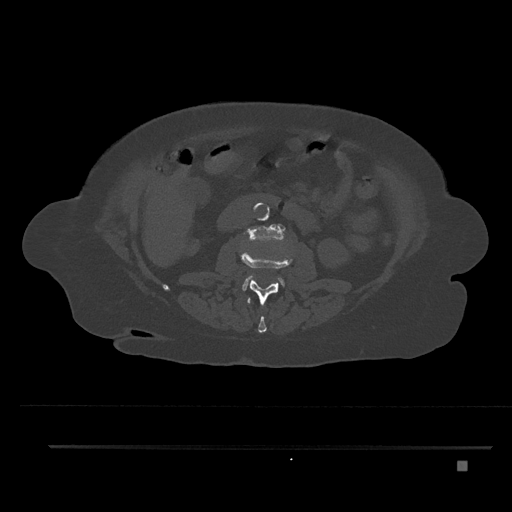
CT including the spine, one axial slice; position 167 of 797 along the scan axis; bone window (W 1800 / L 400 HU); 0.5 mm slice thickness; 512 × 512 image matrix, field of view 437 × 437 mm. Female patient, age 76 years. From the clinical record (not read from this slice): primary cancer: lung.
Structures marked on this image (semi-automatically segmented with operator editing):
- L1 vertebra: bounding box [x1, y1, x2, y2] px = [247, 298, 267, 333]
- L2 vertebra: [240, 243, 293, 306]
- L3 vertebra: [243, 224, 285, 290]